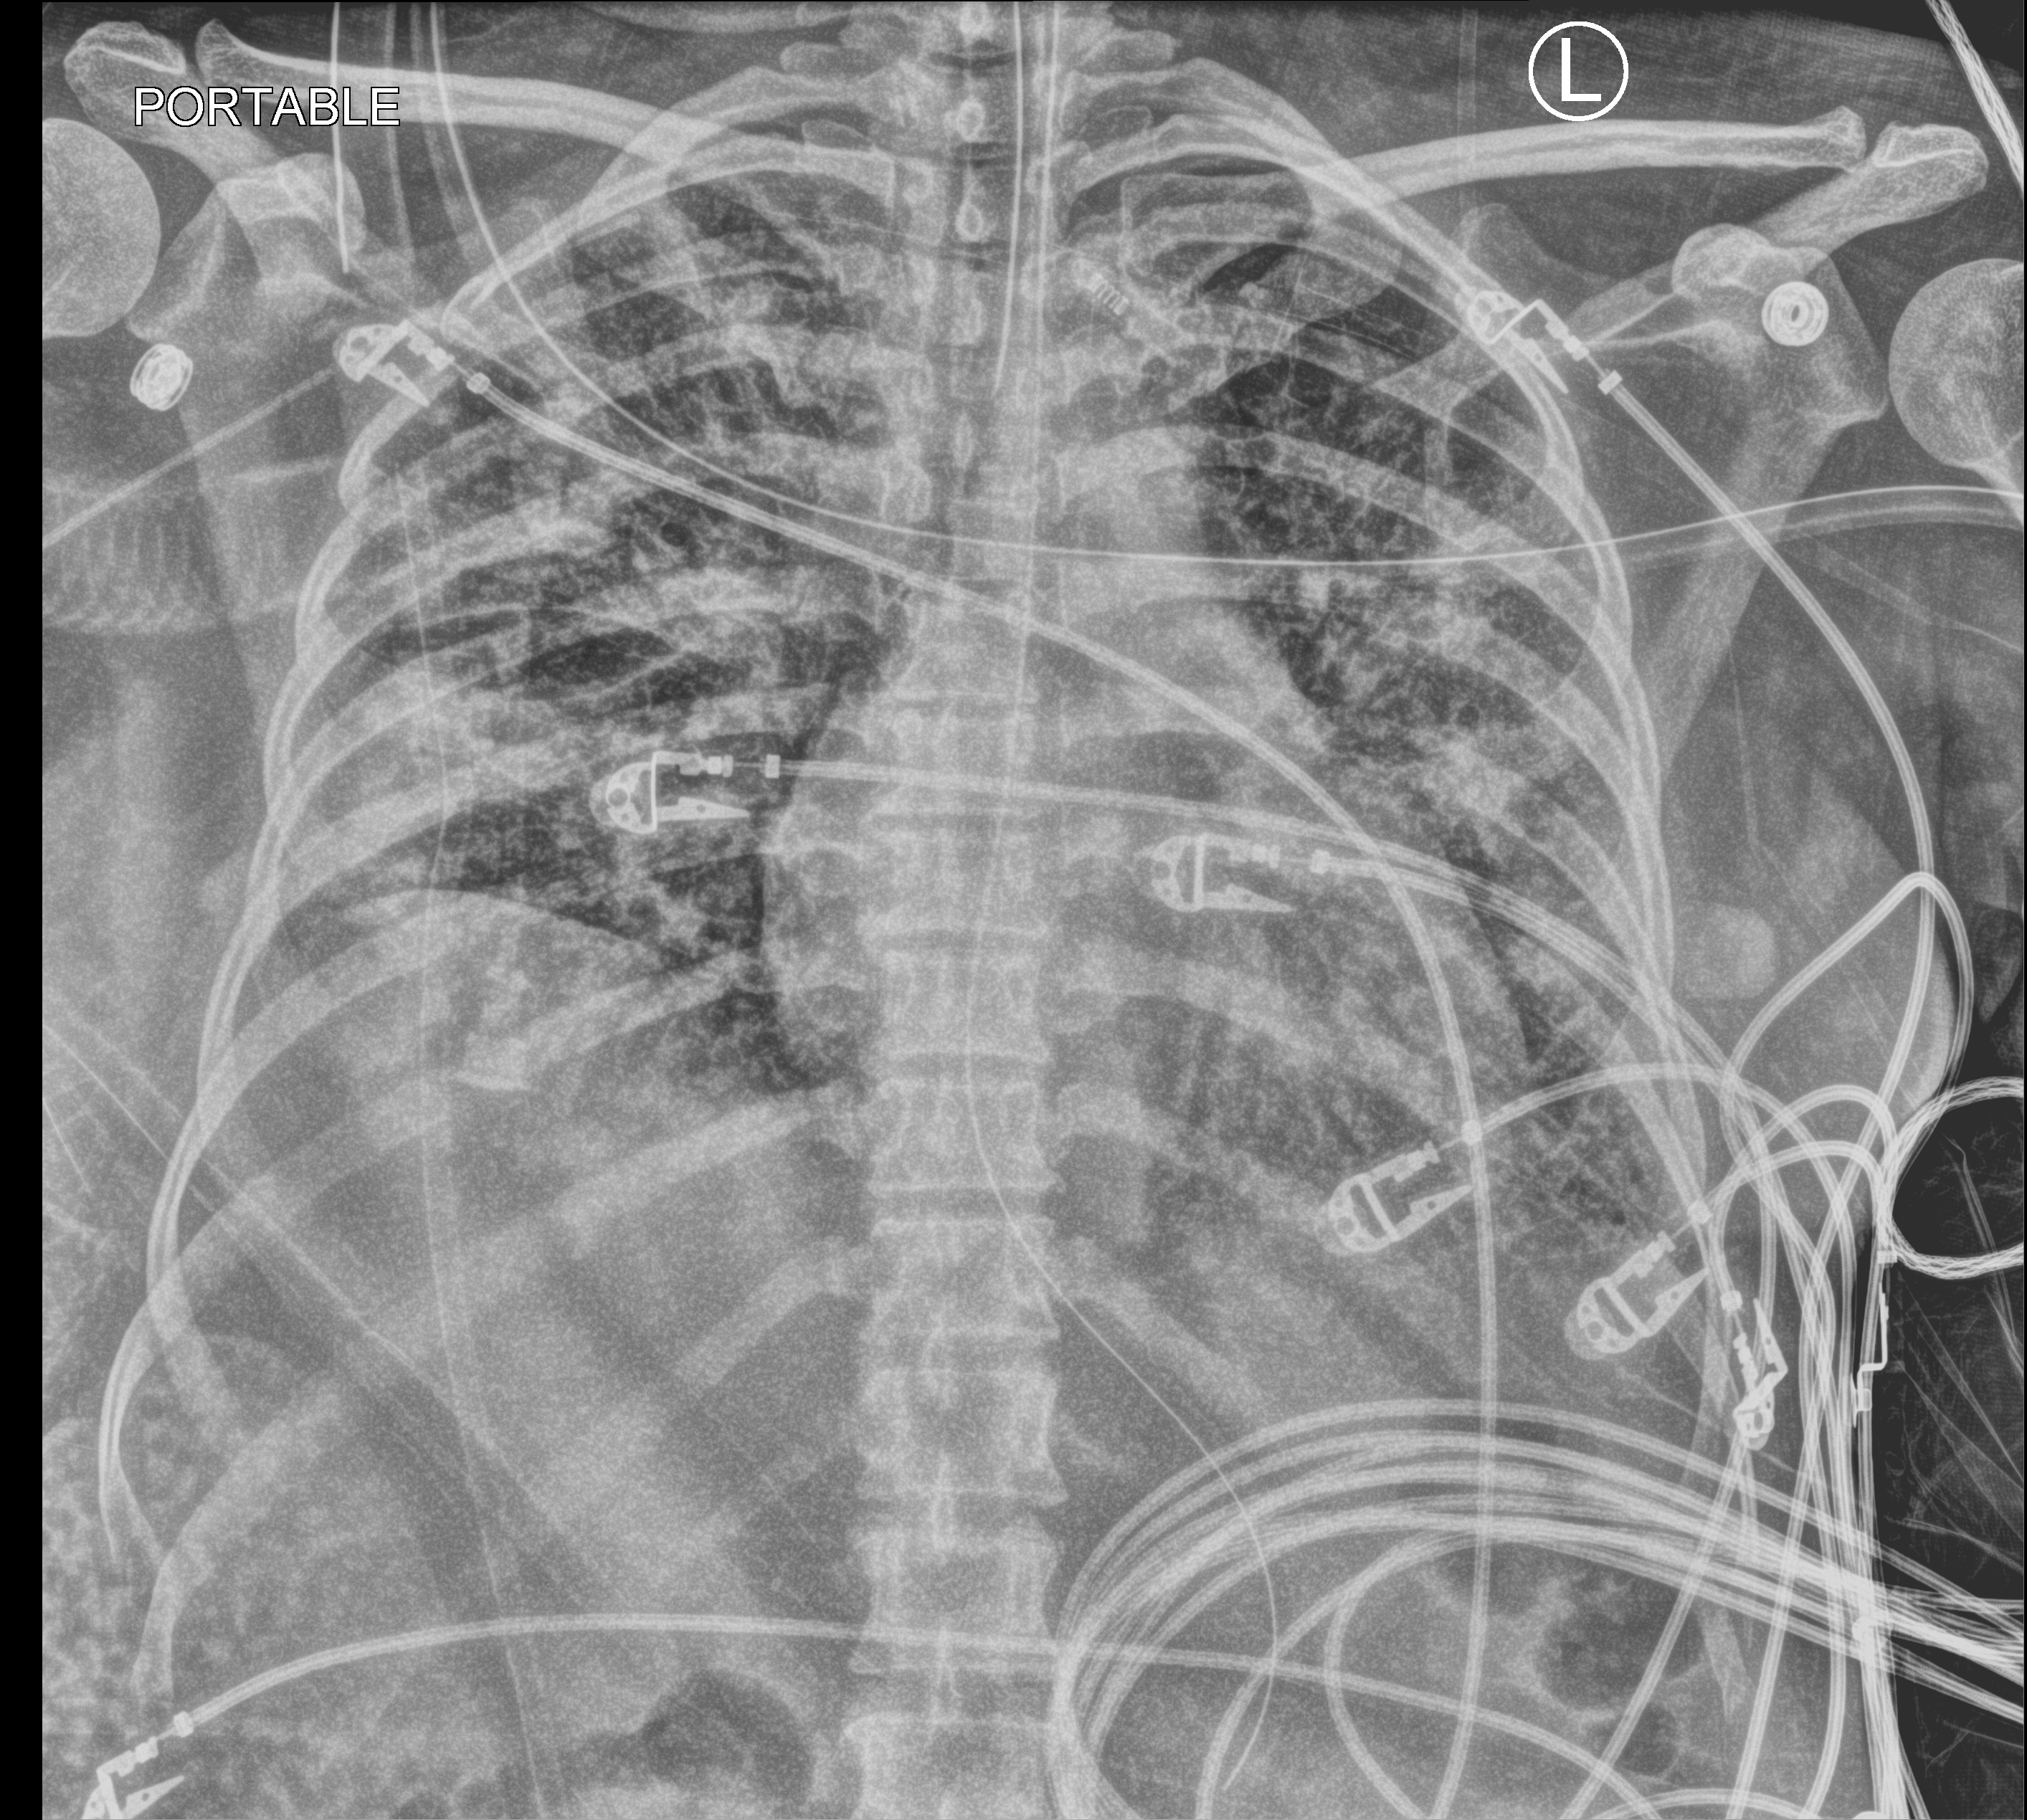
Portable chest radiograph; anteroposterior (AP) projection. Patient hospitalised with COVID-19; female, aged 18–59 years.
Admission-level facts for this patient (not findings on this image; timing relative to this image not recorded): COPD (admission record): no; length of hospital stay: 71 days.